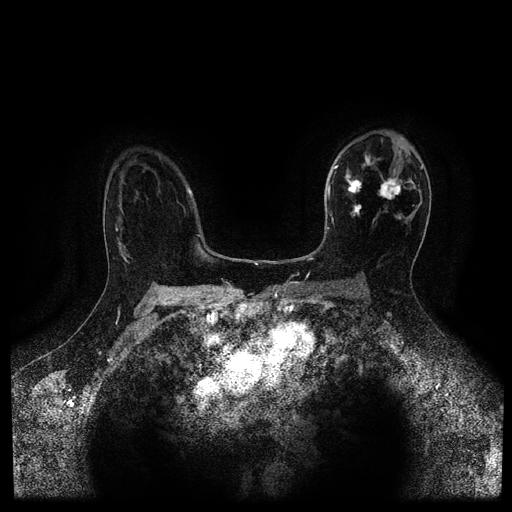
Breast MRI (dynamic contrast-enhanced, multi-phase), one axial slice; position 68 of 116 along the scan axis; dynamic contrast-enhanced series, time point 2 of 5 at this slice position (early post-contrast); 1.5 T; TE 2.7 ms, TR 5.4 ms; 512 × 512 image matrix, field of view 340 × 340 mm. Female patient, age 50 years.
Annotated regions visible in this slice (semi-automatically segmented with operator editing):
- breast lesion (labelled 'tumour' in the annotation; benign lesions carry a separate 'benign' label): bounding box (x1, y1, x2, y2) in pixels: (344, 172, 405, 218)
- breast lesion (labelled 'tumour' in the annotation; benign lesions carry a separate 'benign' label): (363, 155, 373, 166)